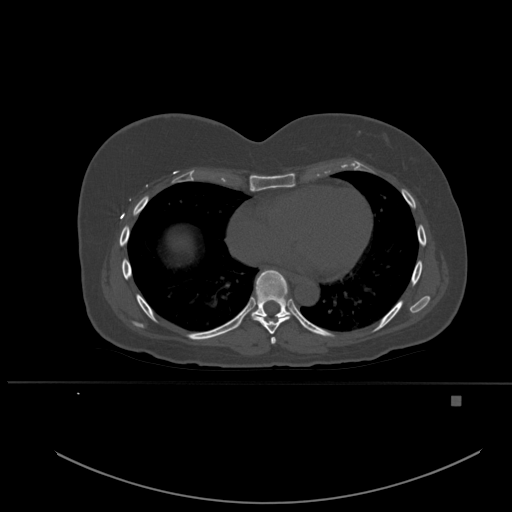
CT including the spine, one axial slice. Position 328 of 651 along the scan axis. Bone window (W 1800 / L 400 HU). 1.5 mm slice thickness. 512 × 512 image matrix. Female patient, age 49 years. Case-level facts recorded for this patient, not image findings: primary cancer: breast; vertebrae with lytic lesions (as recorded): L3, T12, L4.
Annotated regions visible in this slice (semi-automatic segmentation, software-assisted and operator-edited):
- T6 vertebra: bounding box <271,337,276,344> (left, top, right, bottom; pixels)
- T7 vertebra: <252,303,290,334>
- T8 vertebra: <239,270,295,325>